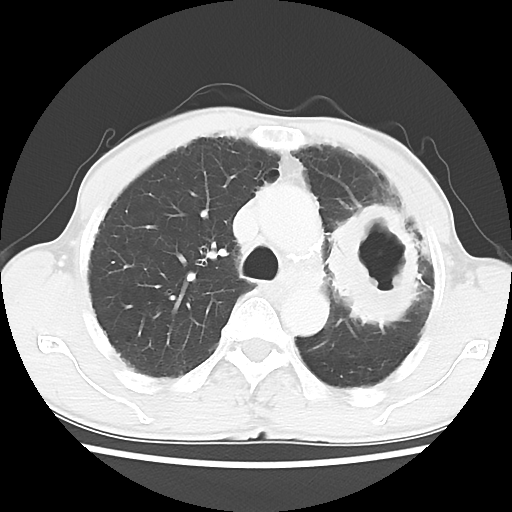
Chest CT, one axial slice; position 42 of 60 along the scan axis; 120 kVp; lung window (W 1500 / L -600 HU); 512 × 512 image matrix, field of view 308 × 308 mm. Patient: male, 64 years. From the clinical record (not read from this slice): clinical TNM (as recorded): T3 N3 M0.
Structures marked on this image (rectangle marked by the reading radiologist):
- lung tumour (recorded histology: adenocarcinoma): bounding box [x1, y1, x2, y2] px = [313, 196, 425, 336]